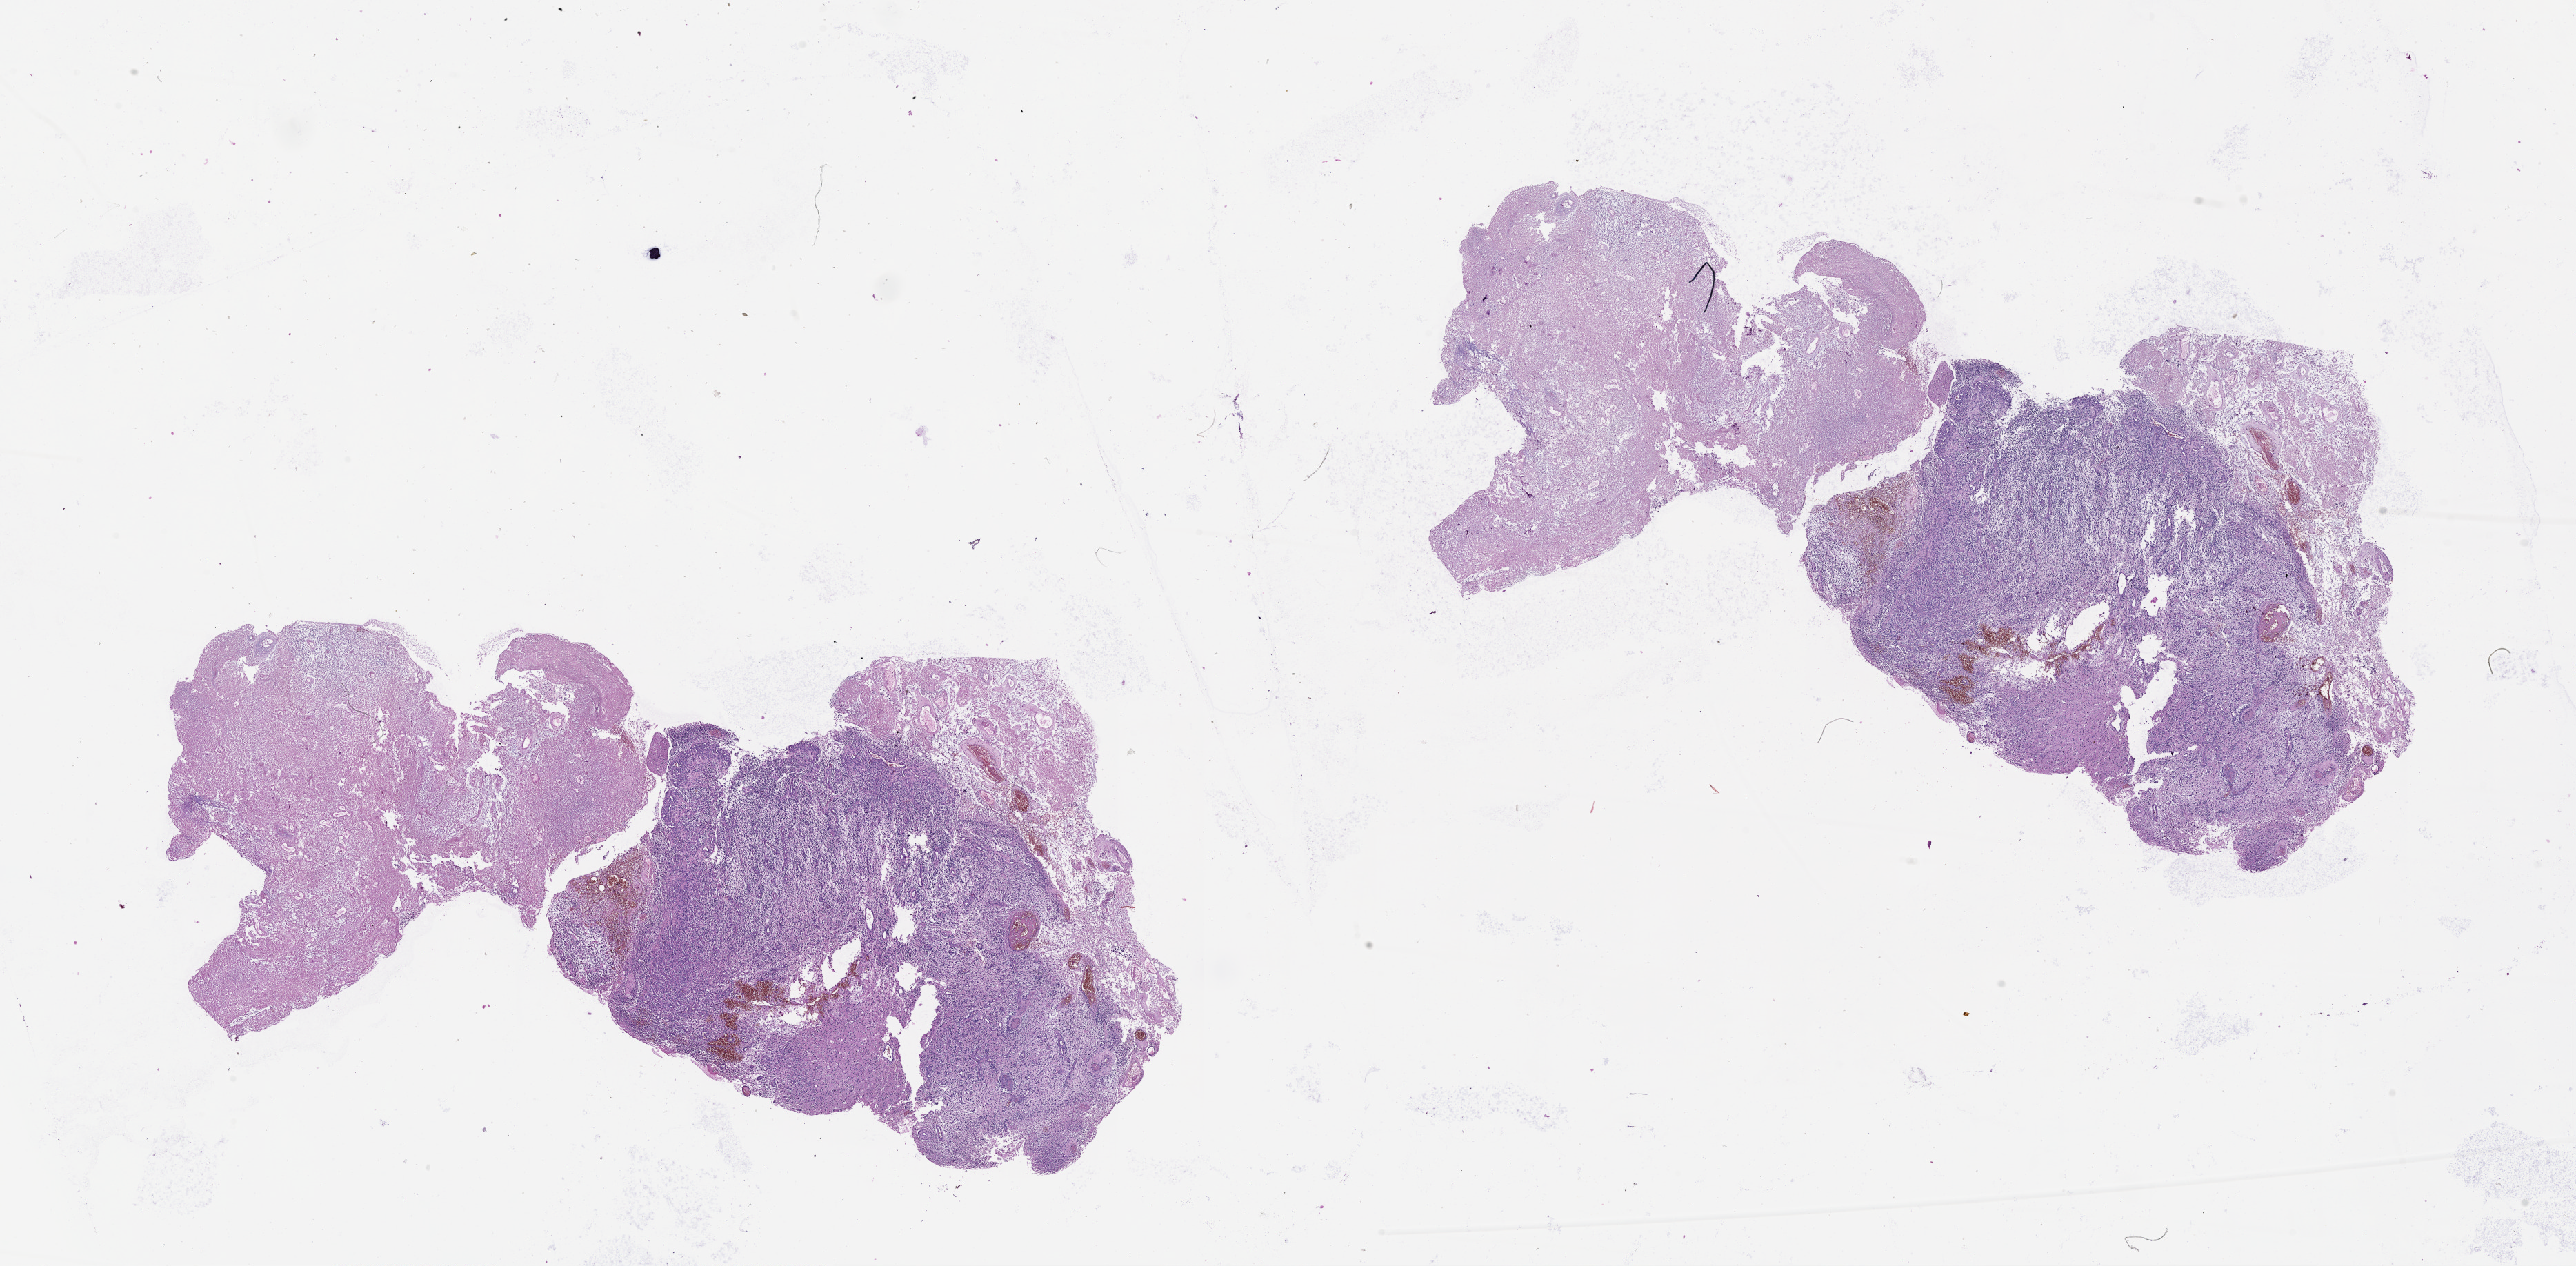
H&E whole-slide image — whole scanned area (about 30.1 x 14.8 mm) shown as a low-resolution overview; tumour tissue sample, brain. Male, 65 y/o.
* primary tumour site (as recorded): parietal lobe
* histologic diagnosis: Glioblastoma